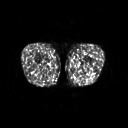
FDG PET of an extremity soft-tissue mass (from a PET/CT study), one axial slice. Position 213 of 267 along the scan axis. 3.27 mm slice thickness. 128 × 128 image matrix, field of view 500 × 500 mm. Patient: male, 27 years. Case-level facts recorded for this patient, not image findings: histological type: extraskeletal osteosarcoma; grade: high; site of the primary tumour: left adductur.
Annotated regions visible in this slice (expert contour drawn on MRI and transferred to this co-registered scan by the dataset authors):
- gross tumour volume (mass): bounding box <82,64,87,67> (left, top, right, bottom; pixels)